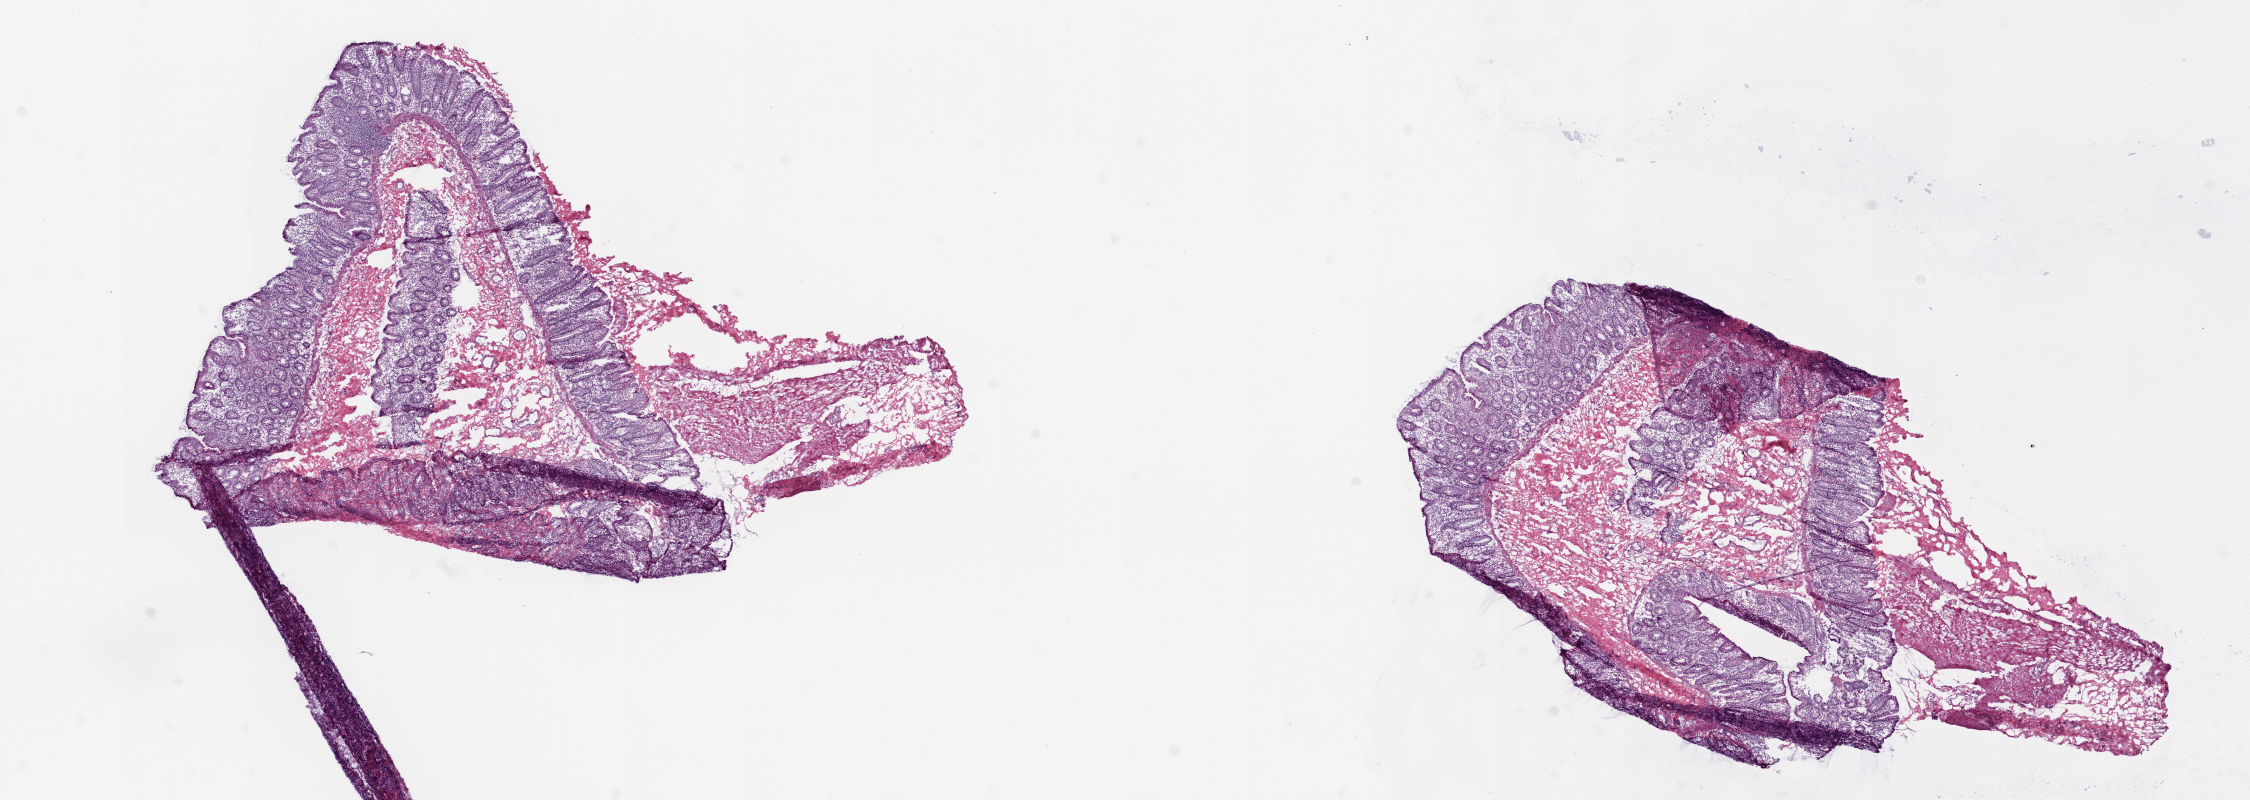
H&E-stained whole-slide image — whole scanned area (about 18.1 x 6.4 mm) shown as a low-resolution overview; frozen section from the top of the tissue portion; sample: solid tissue normal (non-tumour tissue), colon. Patient: male, age at initial diagnosis 68 years.
This section: solid tissue normal (non-tumour) sample from the same patient. Patient diagnosis: Adenocarcinoma, NOS.